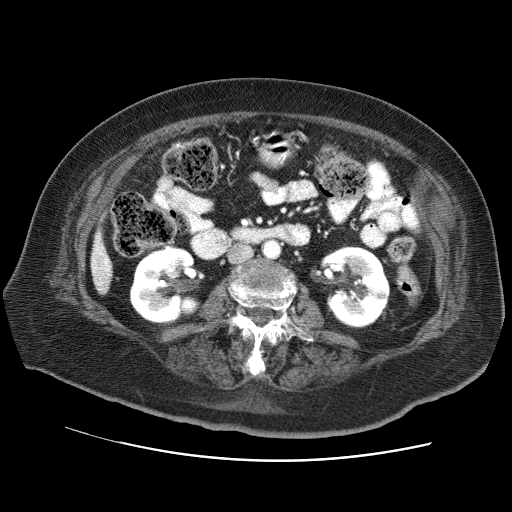
Contrast-enhanced abdominal CT (liver protocol), one axial slice. Position 16 of 73 along the scan axis. Reconstruction kernel STANDARD. Soft-tissue window (W 400 / L 40 HU). 2.5 mm slice thickness. 512 × 512 image matrix, field of view 380 × 380 mm. Case-level facts recorded for this patient, not image findings: diagnosis: hepatocellular carcinoma (patient treated with transarterial chemoembolisation; whether this scan precedes or follows treatment is not stated here); TNM stage (as recorded): Stage-I; Child-Pugh class: A; tumour differentiation: well differentiated.
Structures marked on this image (semi-automatically segmented with operator editing):
- liver parenchyma outside the tumour (the mass and vessels are separate outlines, so this box may not span the whole liver): box from (x=90, y=229) to (x=112, y=294) px
- liver vessels: (x=95, y=252)–(x=108, y=271)